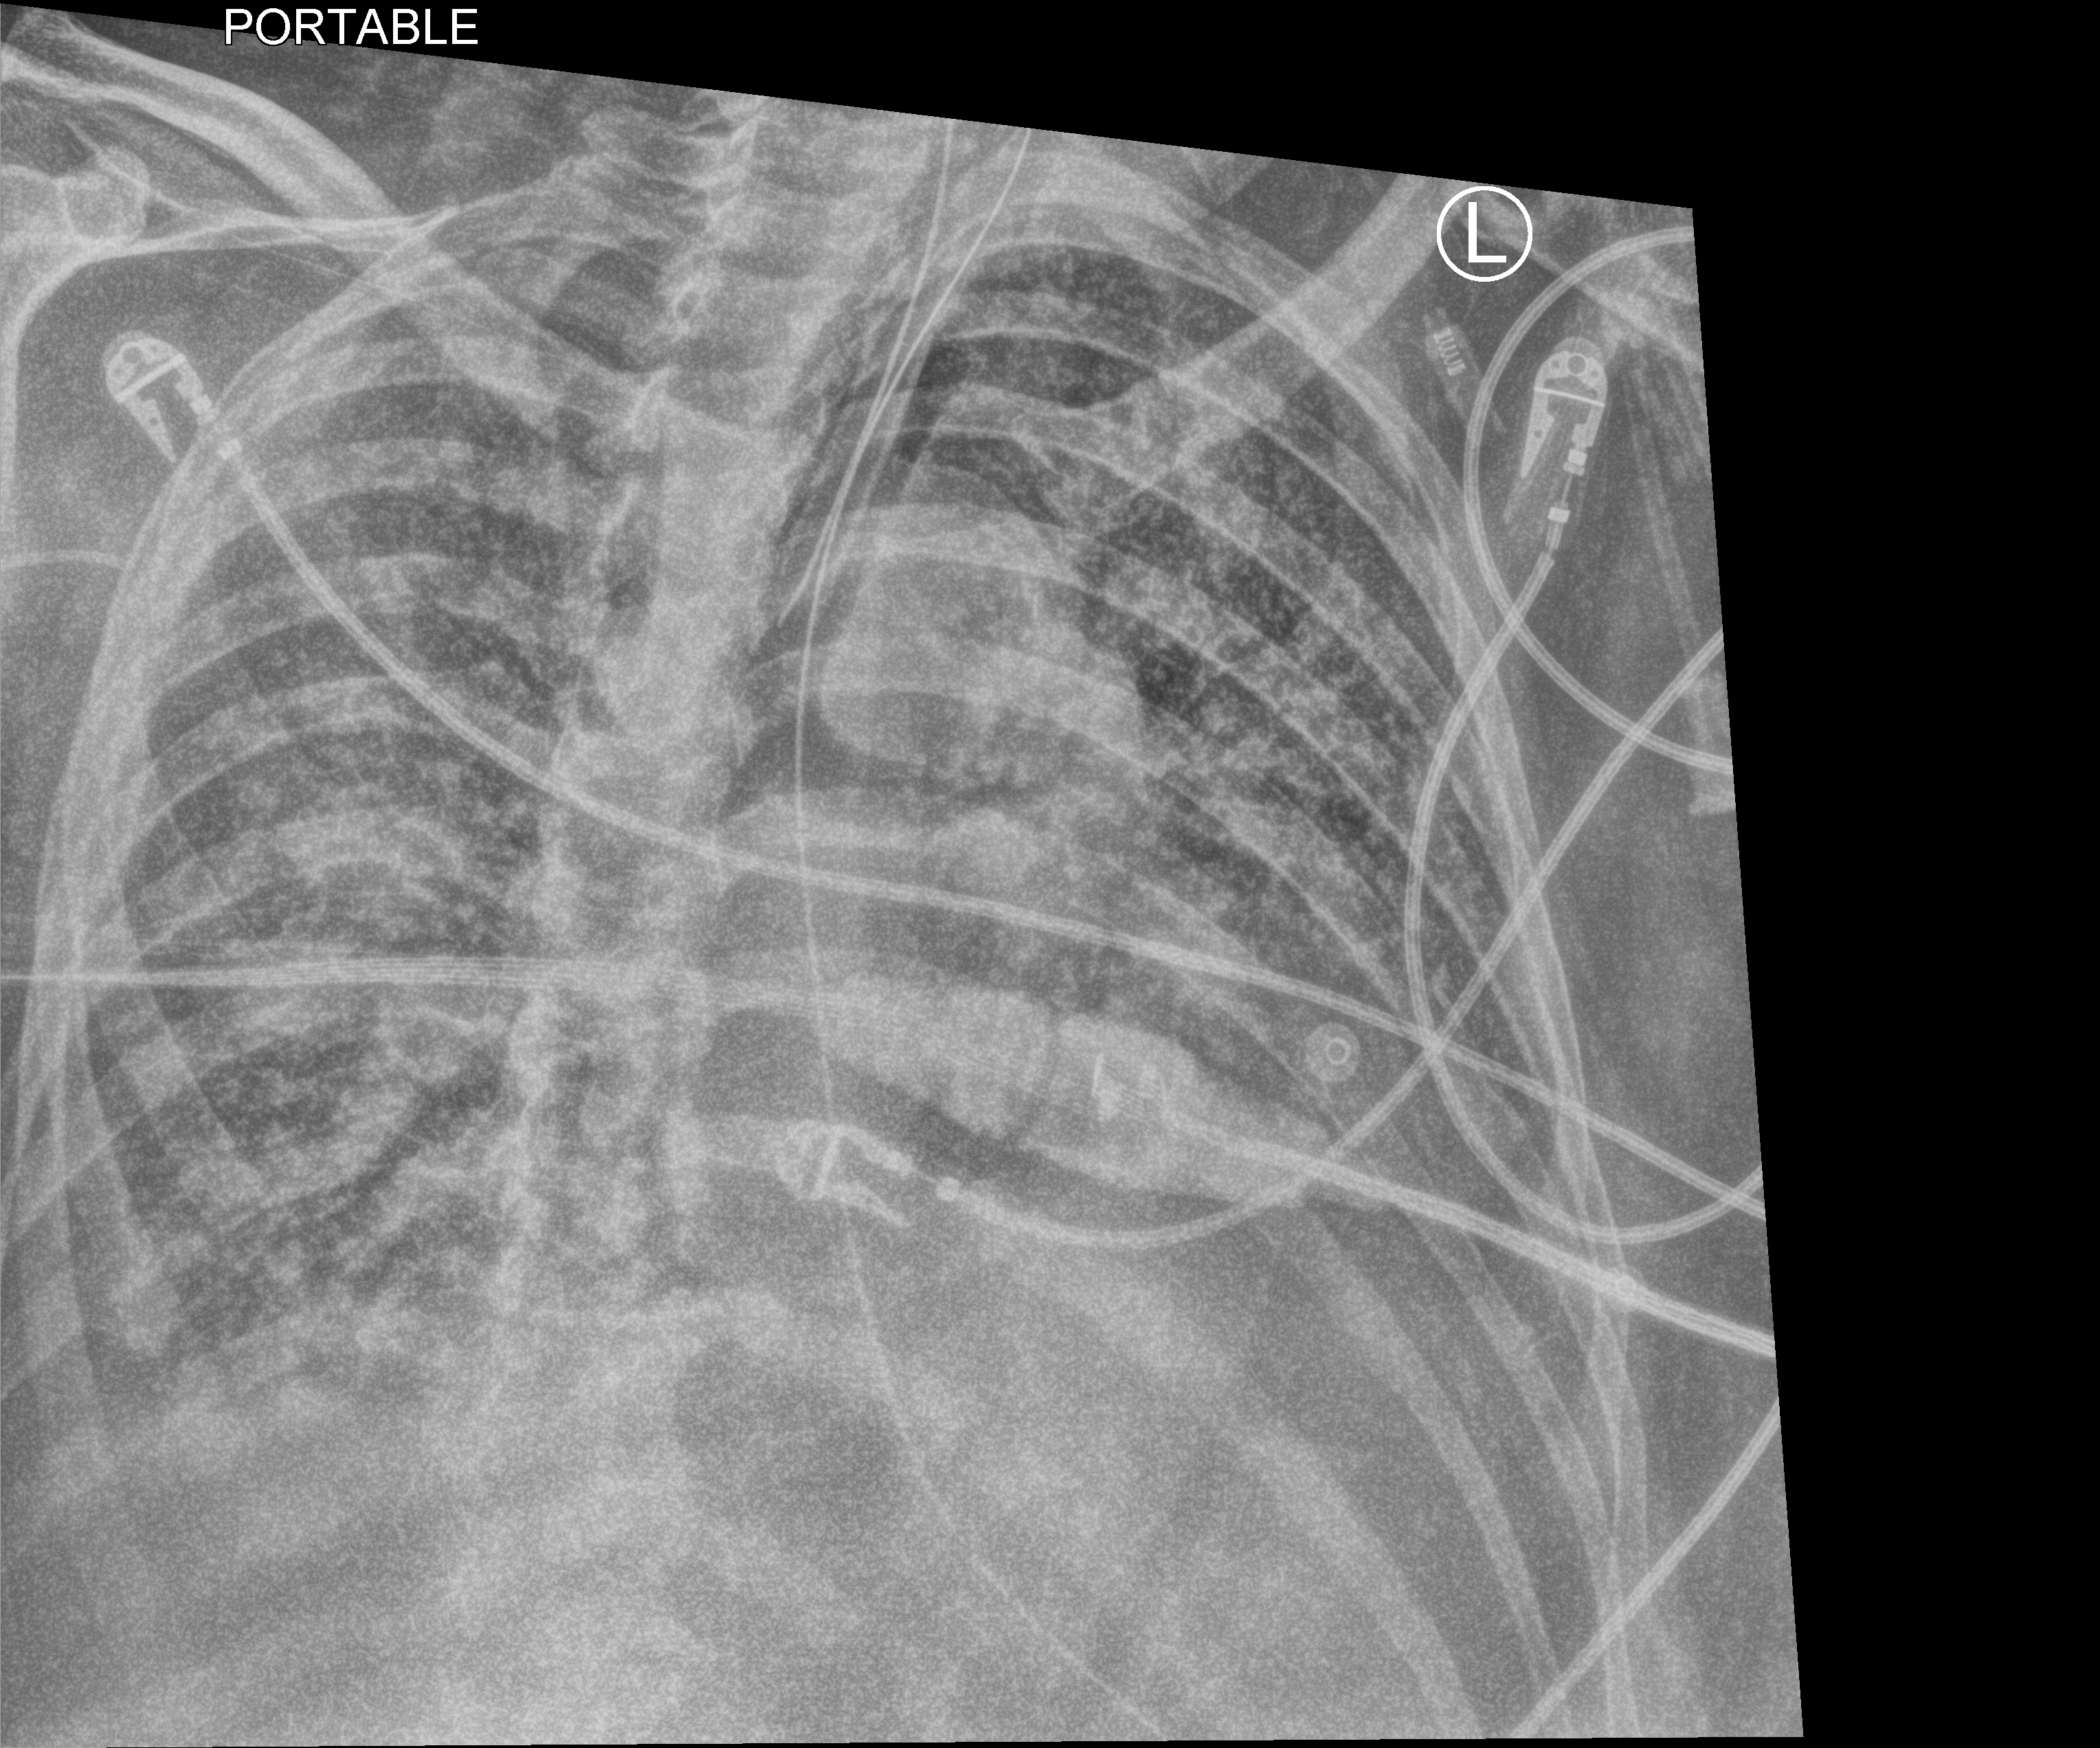
Chest X-ray (portable). Male patient hospitalised with COVID-19, age 60–74 years.
From the hospital-stay record, not from the radiograph (when in the stay this image was taken is not recorded): mechanically ventilated during this hospital stay: yes.